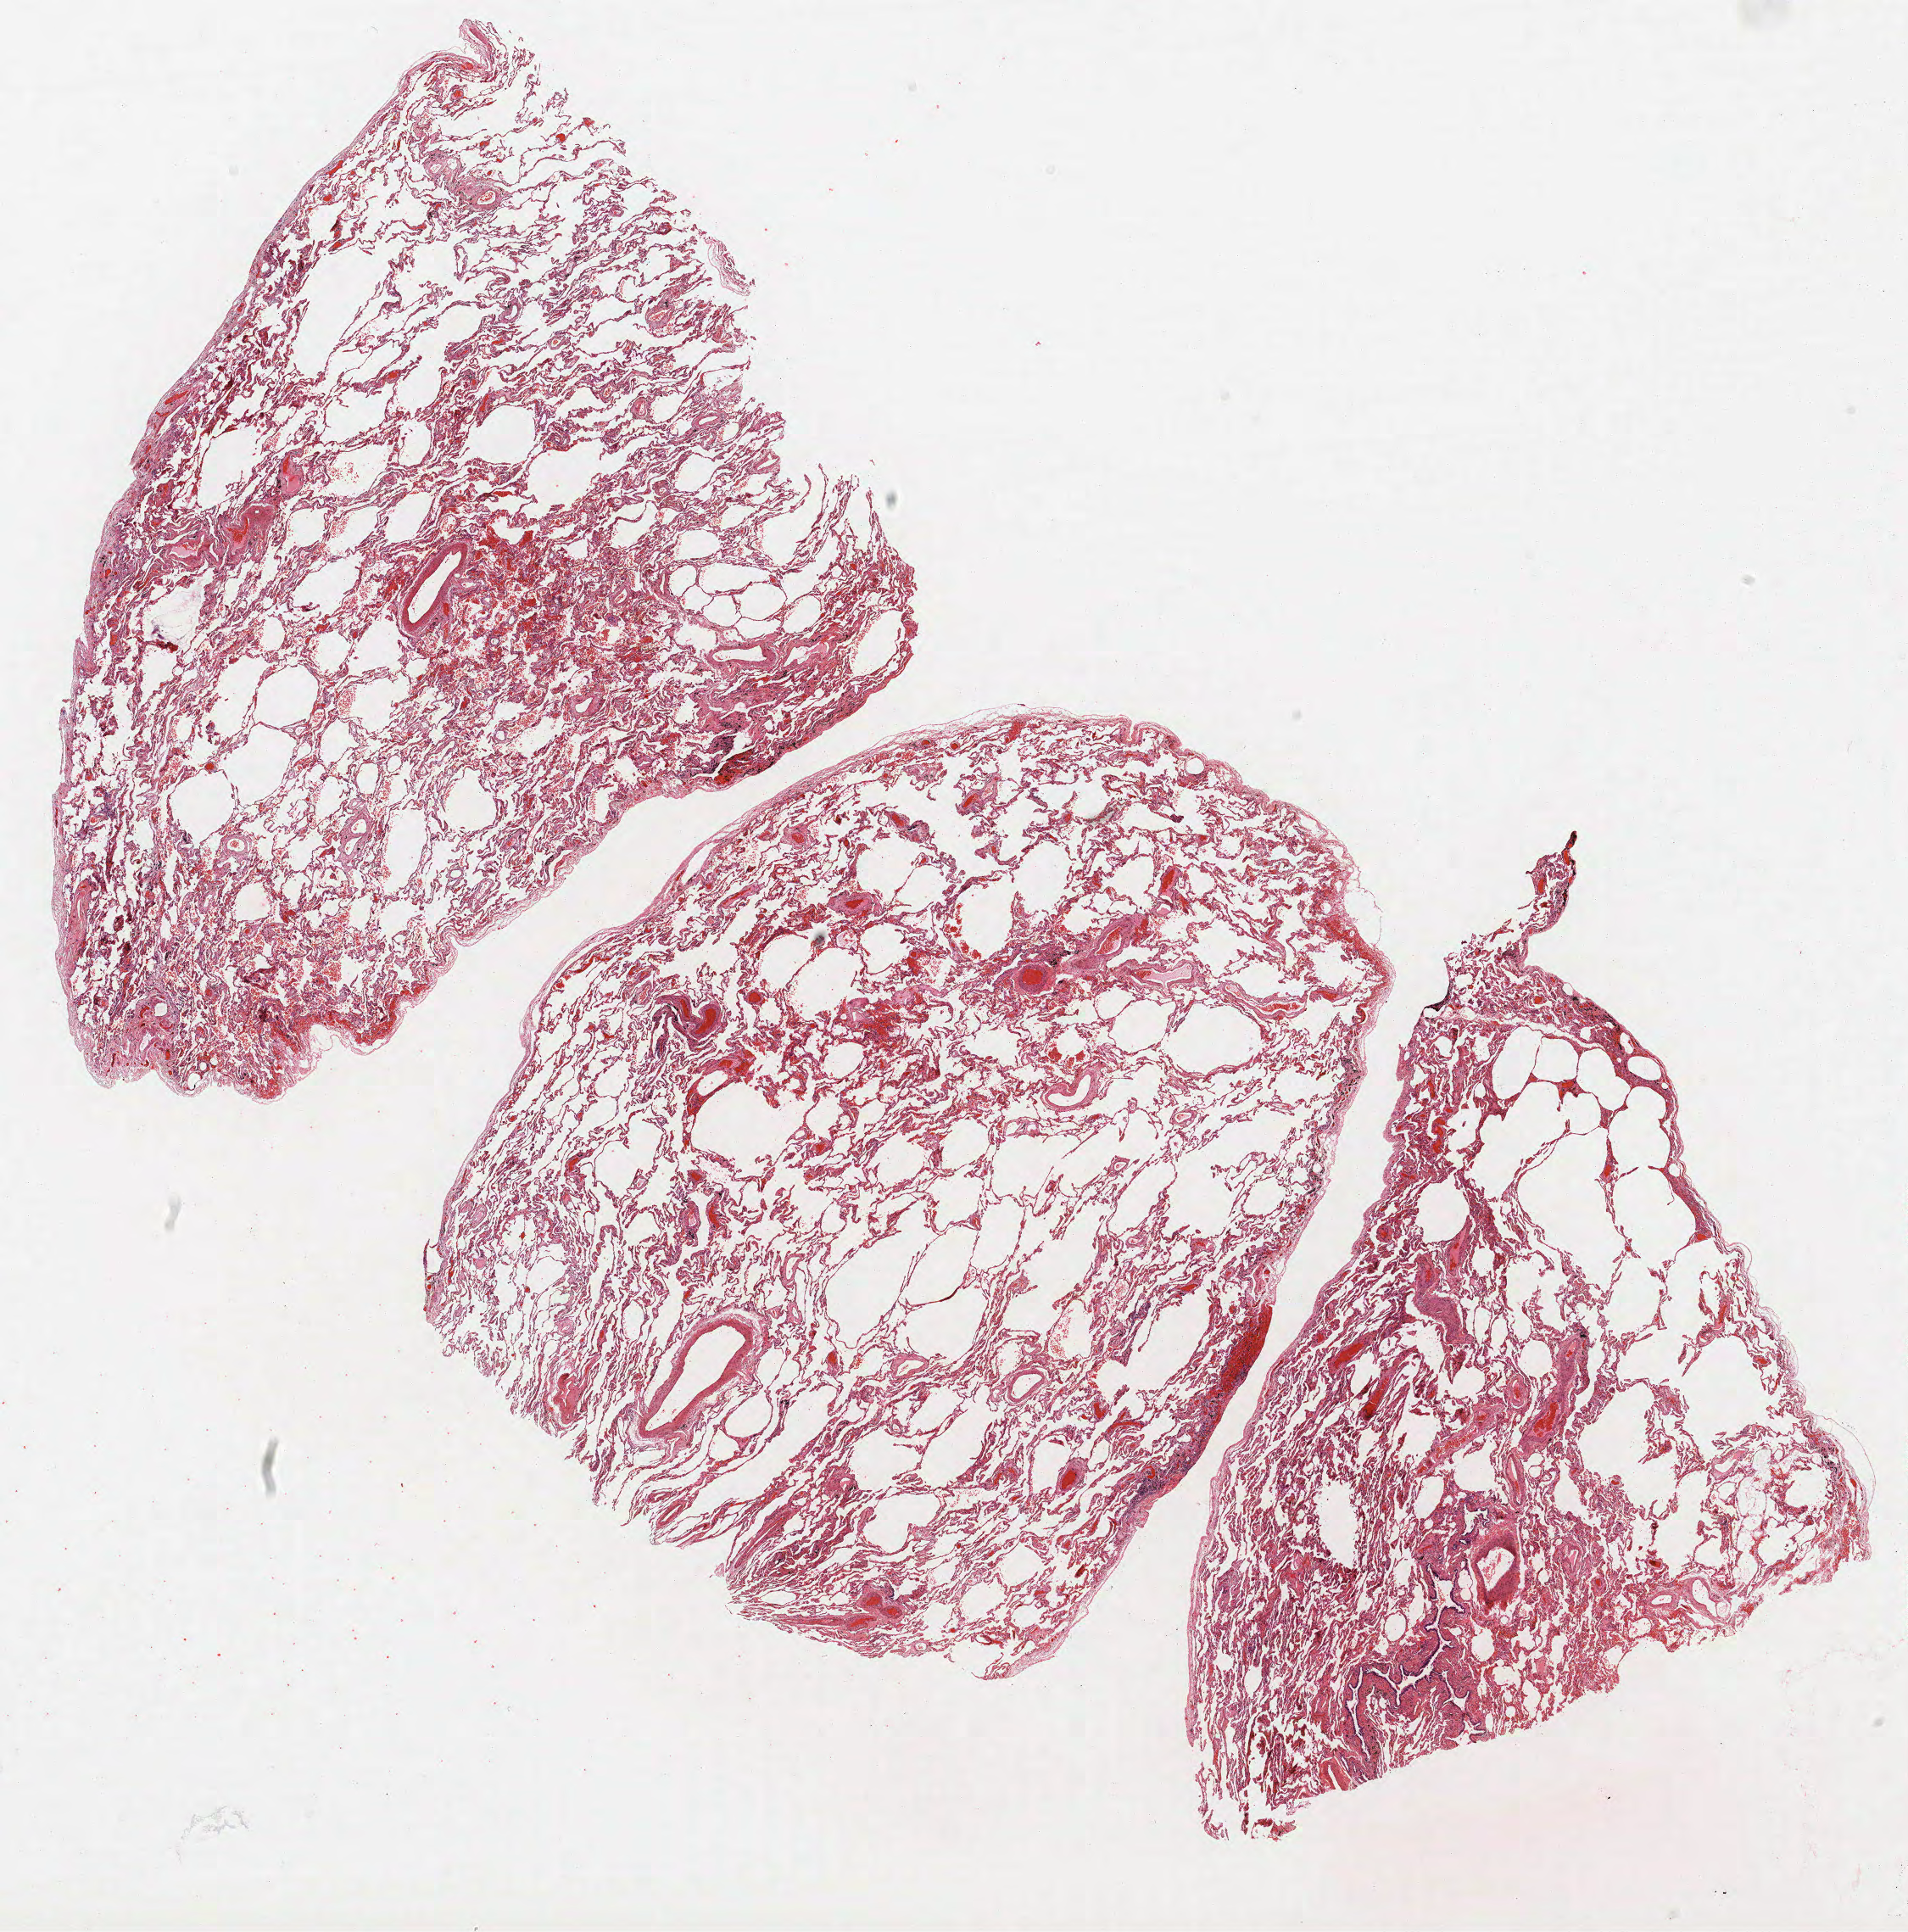
Hematoxylin and eosin (H&E) stained whole-slide image — whole scanned area (about 18.0 x 18.2 mm) shown as a low-resolution overview, FFPE section, lung. Female, age 68 at enrolment. Former smoker at enrolment. Grade: well differentiated (G1).
* primary tumour location (clinical record): right upper lobe, right middle lobe, right lower lobe
* participant's lung-cancer diagnosis: Bronchiolo-alveolar adenocarcinoma, NOS (ICD-O-3 8250/3)
* stage (AJCC 6th edition): IV